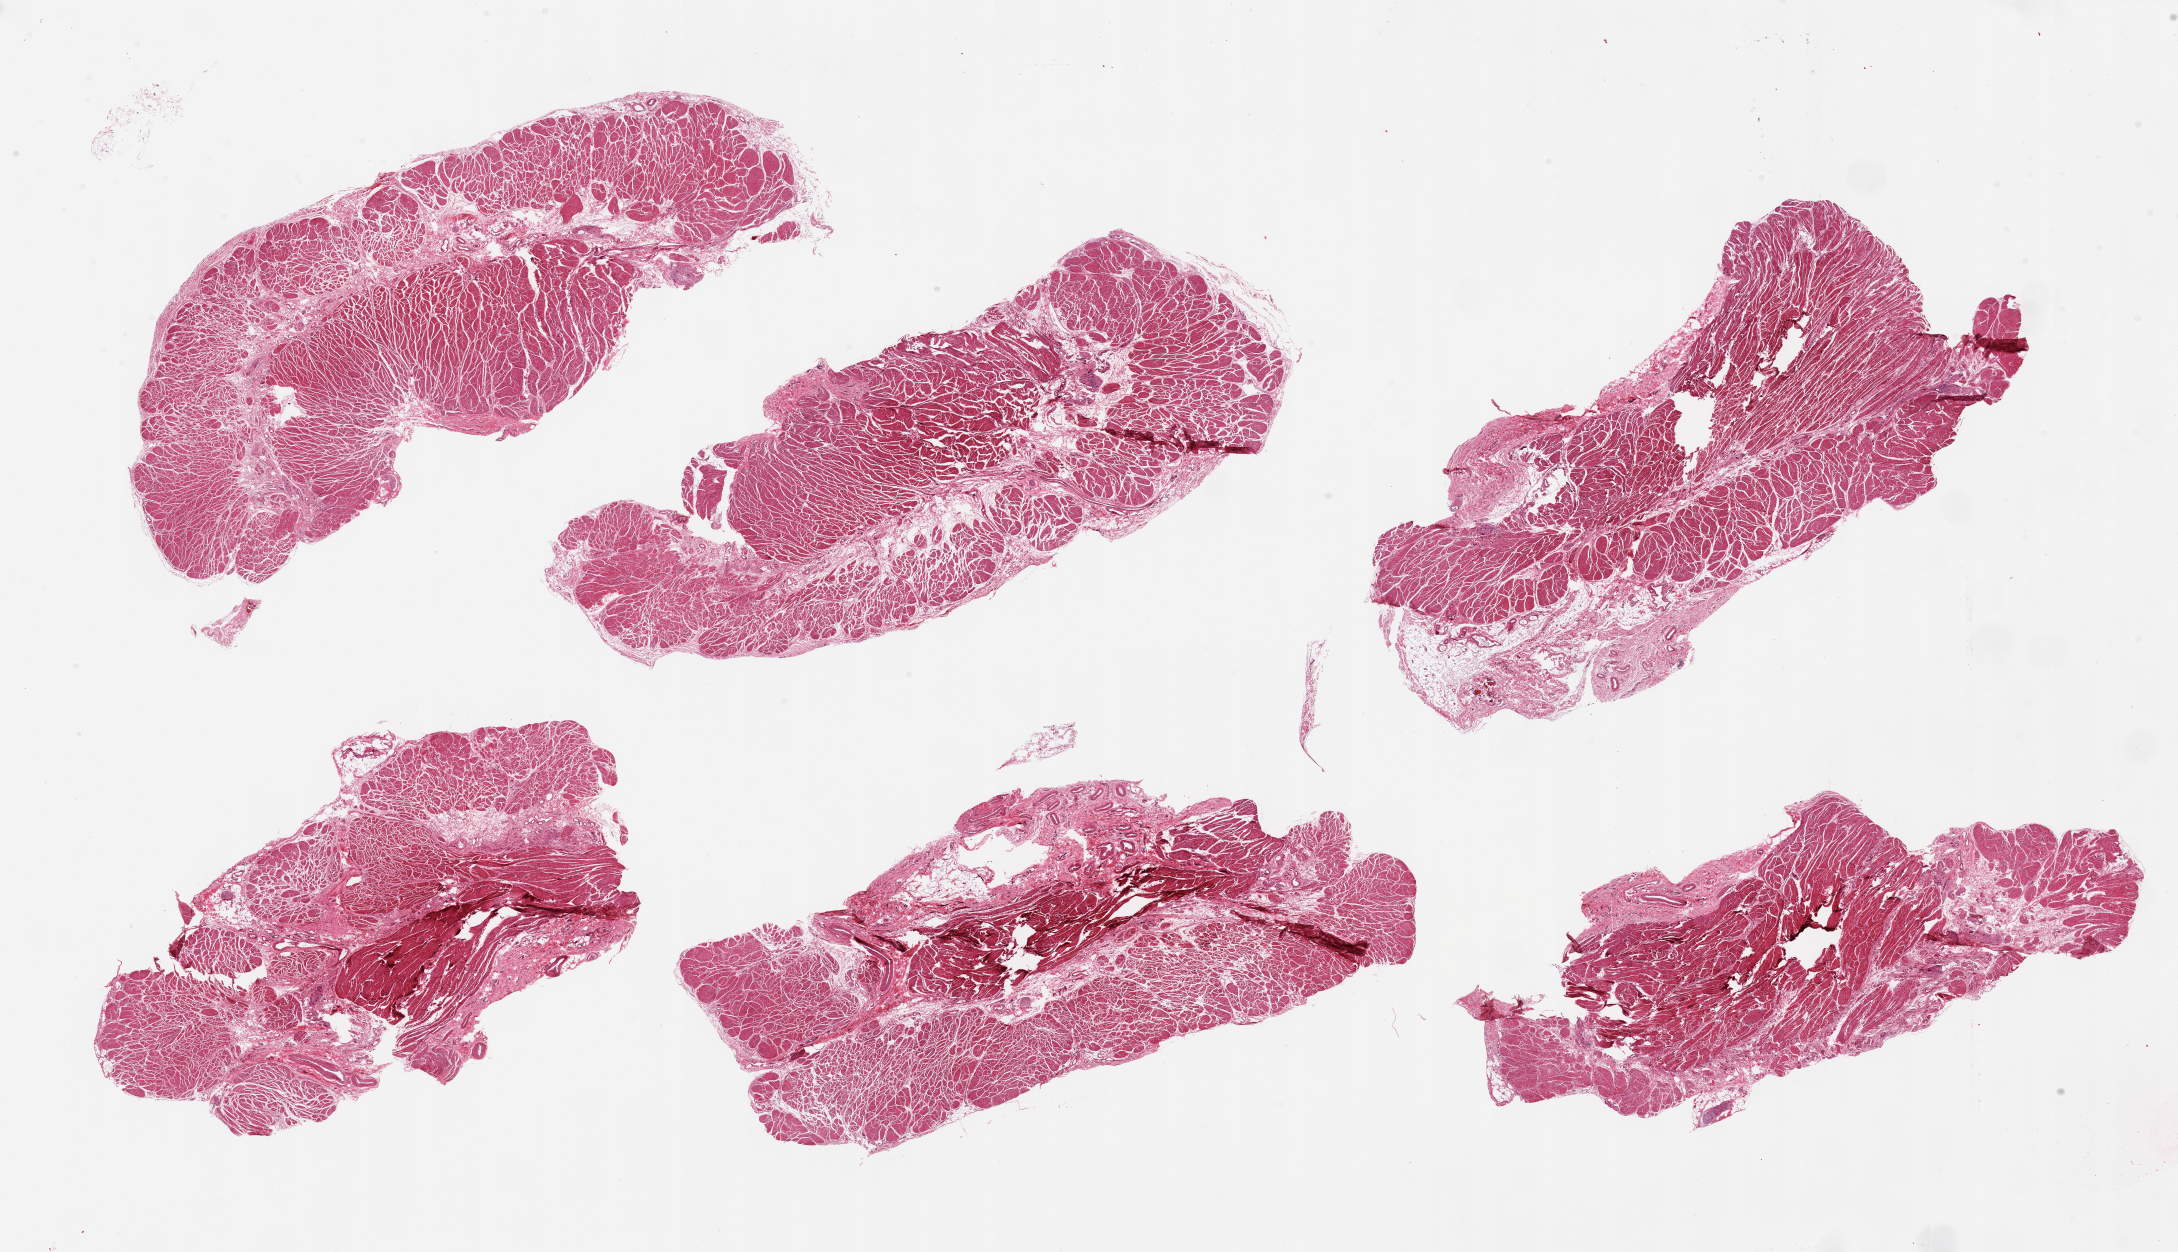
Digitized H&E-stained section, a low-resolution overview of the entire scanned area, about 34.5 x 19.8 mm; PAXgene-fixed paraffin-embedded (PFPE) section; target tissue: gastroesophageal junction; donor tissue sample. Donor: male.
• reviewer comment on this tissue sample: 6 pieces, all target muscularis; trace adherent fat/serosa